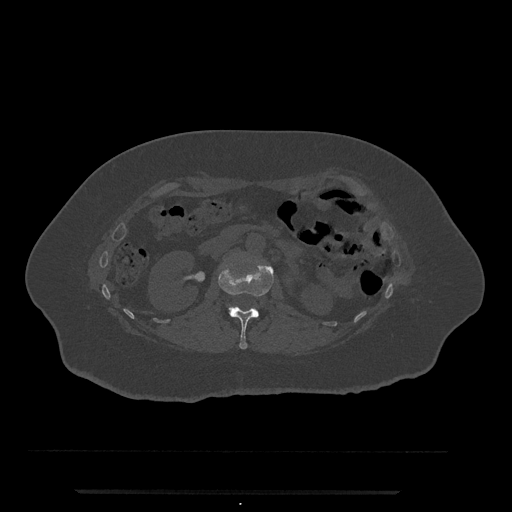
CT including the spine, one axial slice; slice 88 of 797 in the series (ordered by position); reconstruction kernel Br40s/3; 120 kVp; bone window (W 1800 / L 400 HU); 0.5 mm slice thickness; 512 × 512 image matrix, field of view 440 × 440 mm. Patient: female, 51 years. Case-level facts recorded for this patient, not image findings: primary cancer: neuro; vertebrae with lytic lesions (as recorded): T8.
Outlined on this slice (semi-automatically segmented with operator editing):
- L1 vertebra: bounding box [x1, y1, x2, y2] px = [218, 259, 274, 350]
- L2 vertebra: [229, 306, 235, 311]